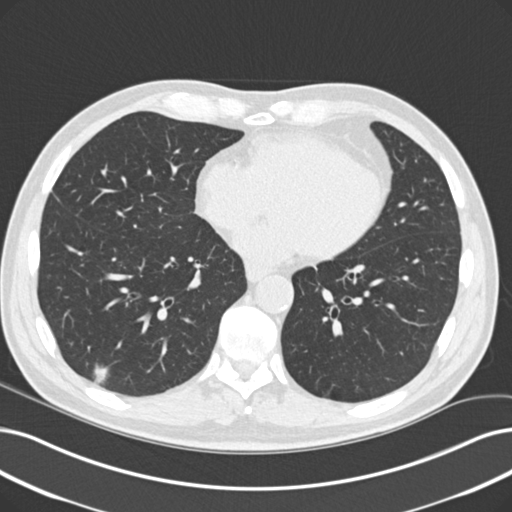
Axial slice from a low-dose chest CT screening exam, baseline screening round, lung window (W 1500 / L -600 HU), standard (soft-tissue) reconstruction kernel (B30f), 120 kVp, slice 139 of 229 in the series, 512 × 512 image matrix, field of view 366 × 366 mm. Male, age 60 years at enrolment.
Expert reader's lesion annotation, bounding box (x1, y1, x2, y2) in pixels: (75, 357, 116, 402). The screening reader recorded 2 non-calcified nodules or masses ≥4 mm on this exam (right lower lobe, left lower lobe); which of them this box marks is not recorded. Official screen result: positive, change unspecified: nodule(s) >= 4 mm or enlarging nodule(s), mass(es), or other non-specific abnormalities suspicious for lung cancer. Later outcome: lung cancer diagnosed 64 days after this screen — acinar cell carcinoma, right lower lobe, moderately differentiated (G2), stage IA (AJCC 6th edition), 16 mm at pathology.